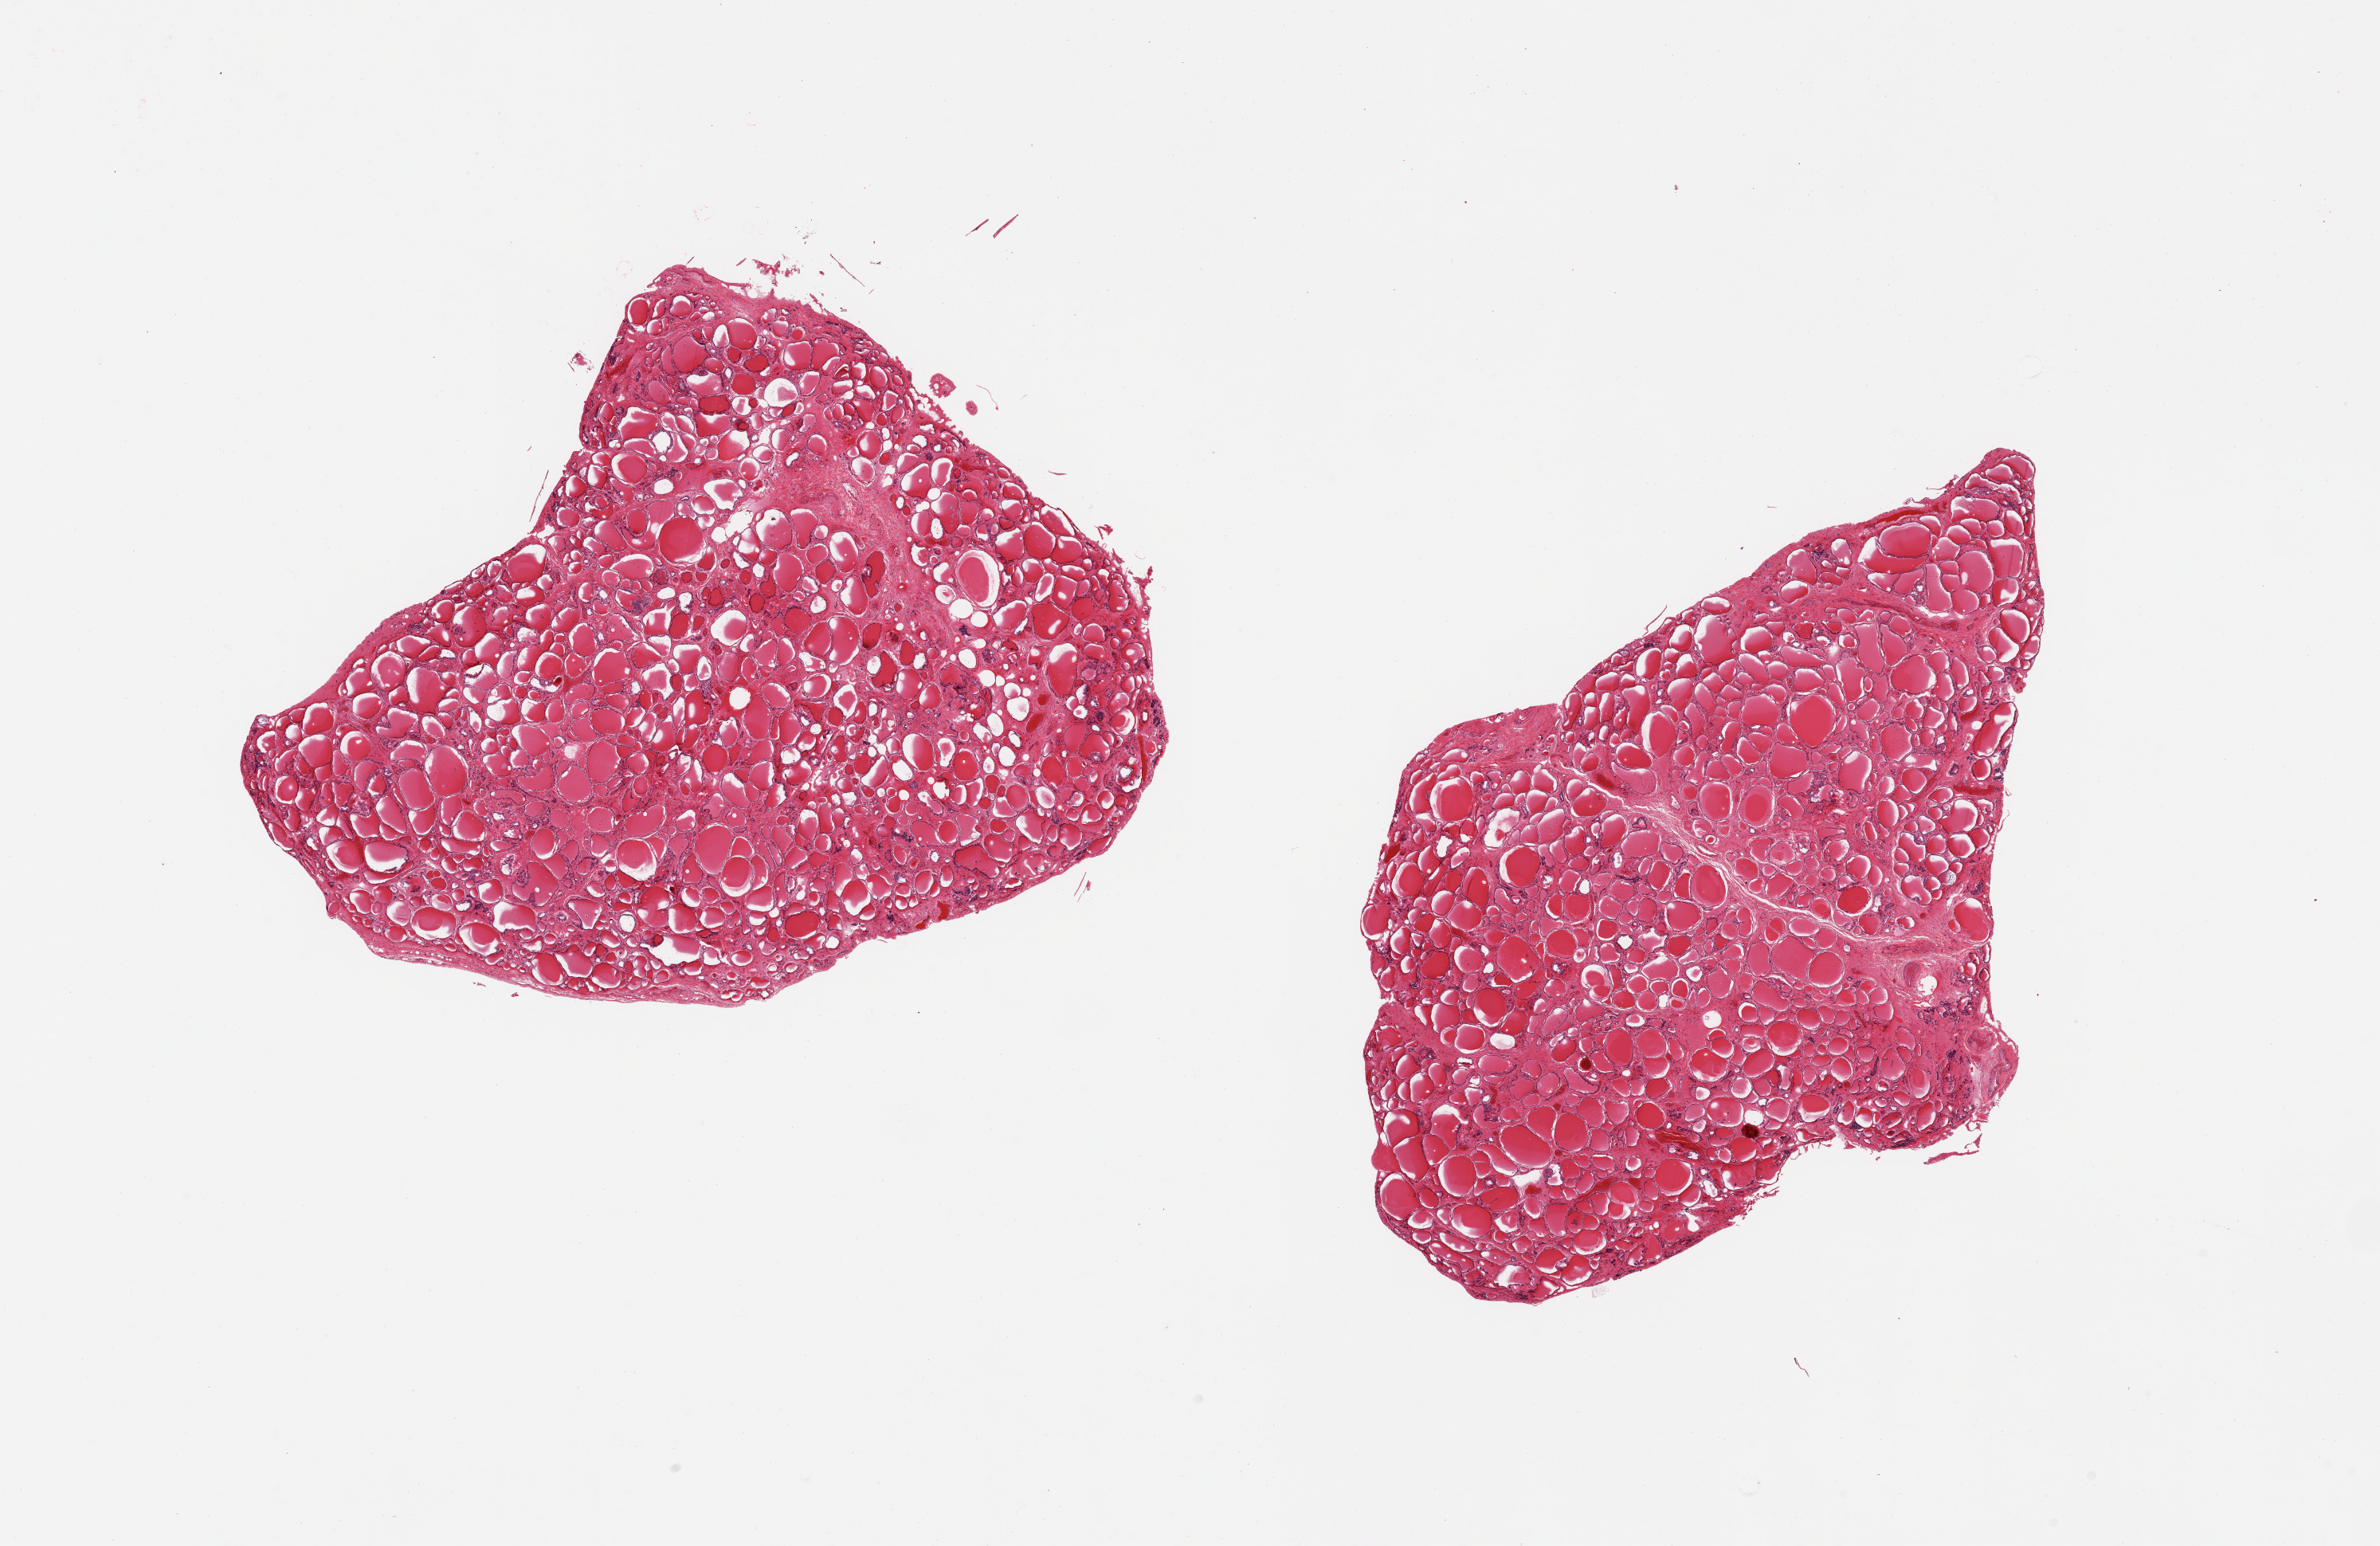
Whole-slide image, haematoxylin and eosin stain — shown as a low-resolution overview of the whole scanned area (about 23.6 x 15.3 mm), PAXgene-fixed paraffin-embedded (PFPE) section, sampled site (target tissue): thyroid, donor tissue sample. Donor sex: male.
* review note (as recorded): 2 pieces